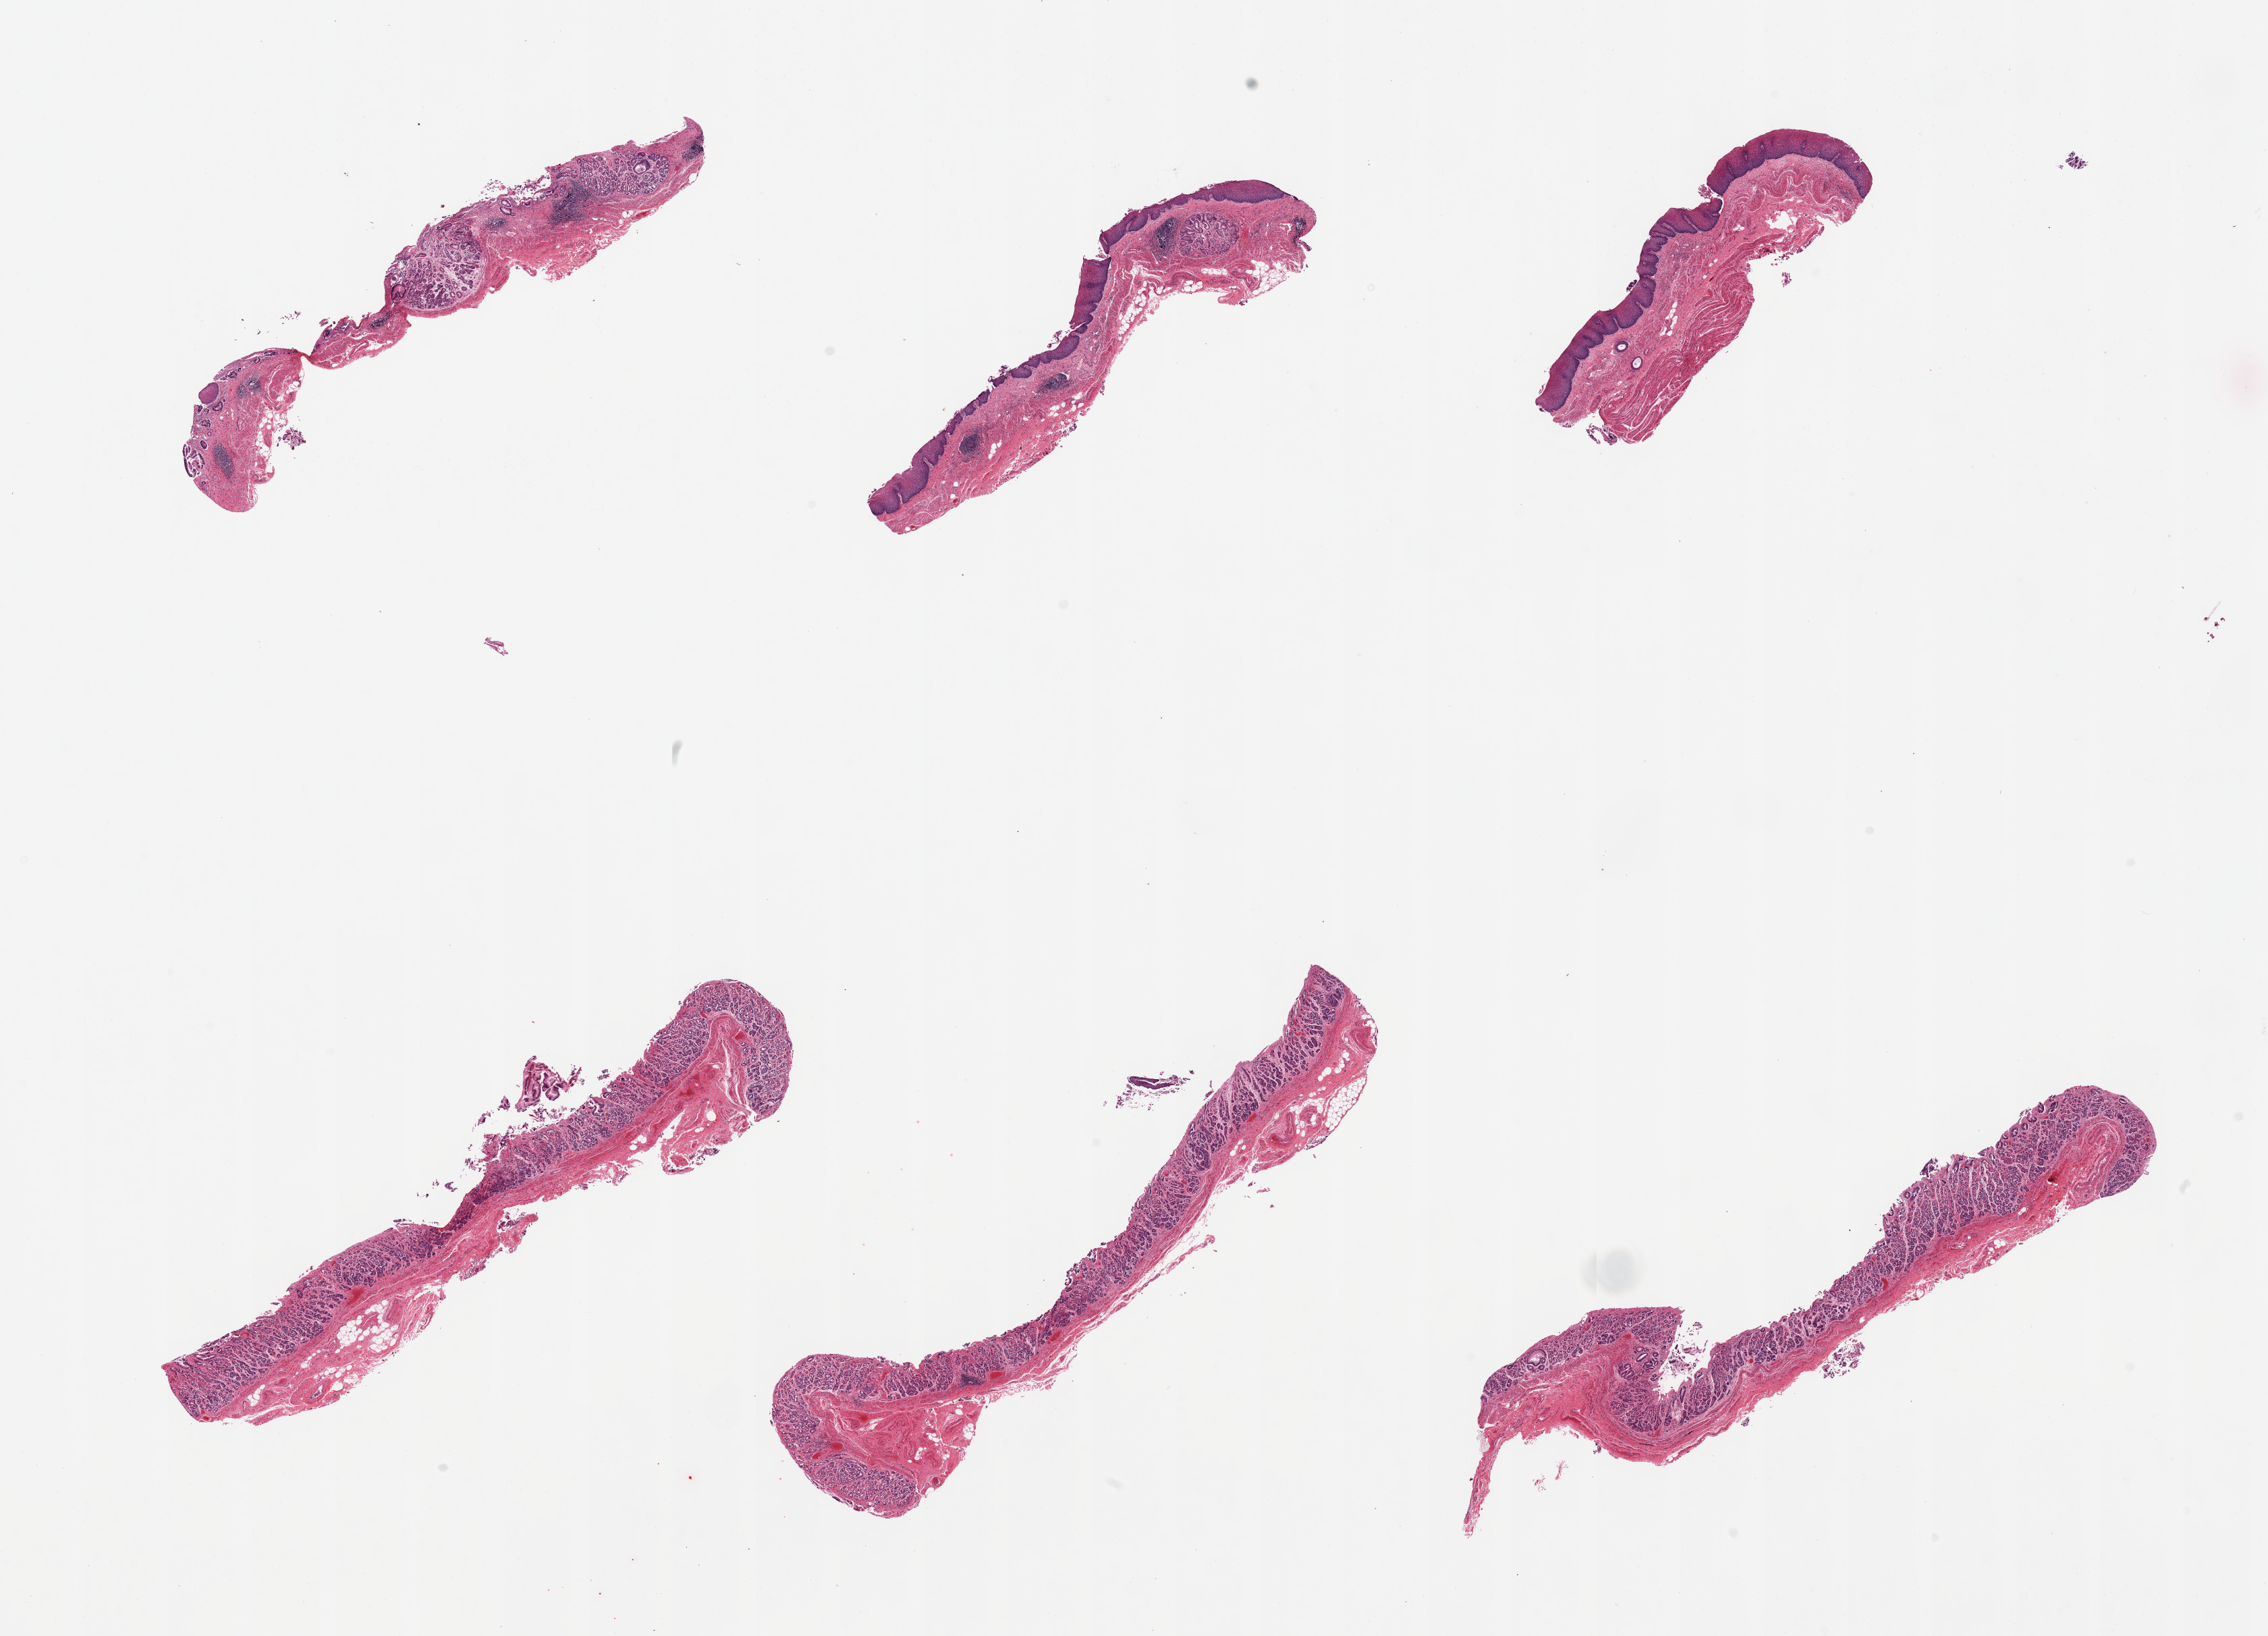
Whole-slide image, H&E stain — shown as a low-resolution overview of the whole scanned area (about 26.6 x 19.2 mm). PAXgene-fixed, paraffin-embedded tissue. Target tissue: esophageal mucous membrane. Tissue donor sample.
• pathologist's review note for this sample: 6 pieces, predominantly include gastric mucosa (not target)